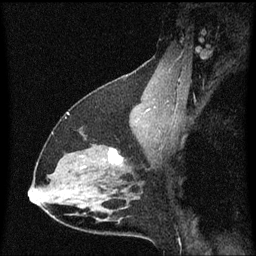
Breast MRI (dynamic contrast-enhanced), one sagittal slice. Slice 40 of 60 in the series (ordered by position). Dynamic contrast-enhanced series, image 2 of 3 at this slice position (ordered by acquisition). 1.5 T. TE 4.2 ms, TR 8.4 ms. 2 mm slice thickness. 256 × 256 image matrix. Patient: female, 38 years. From the clinical record (not read from this slice): setting: breast cancer imaged before/during neoadjuvant chemotherapy; receptor status: HR-positive, HER2-negative.
Outlined on this slice (semi-automatic segmentation, software-assisted and operator-edited):
- analysis volume of interest (the breast-tissue region the enhancement analysis was run in; not a lesion): bounding box (x1, y1, x2, y2) in pixels: (94, 144, 137, 185)
- tumour enhancement mask (voxels above the 70 % enhancement threshold inside the analysis volume of interest): (109, 148, 124, 165)